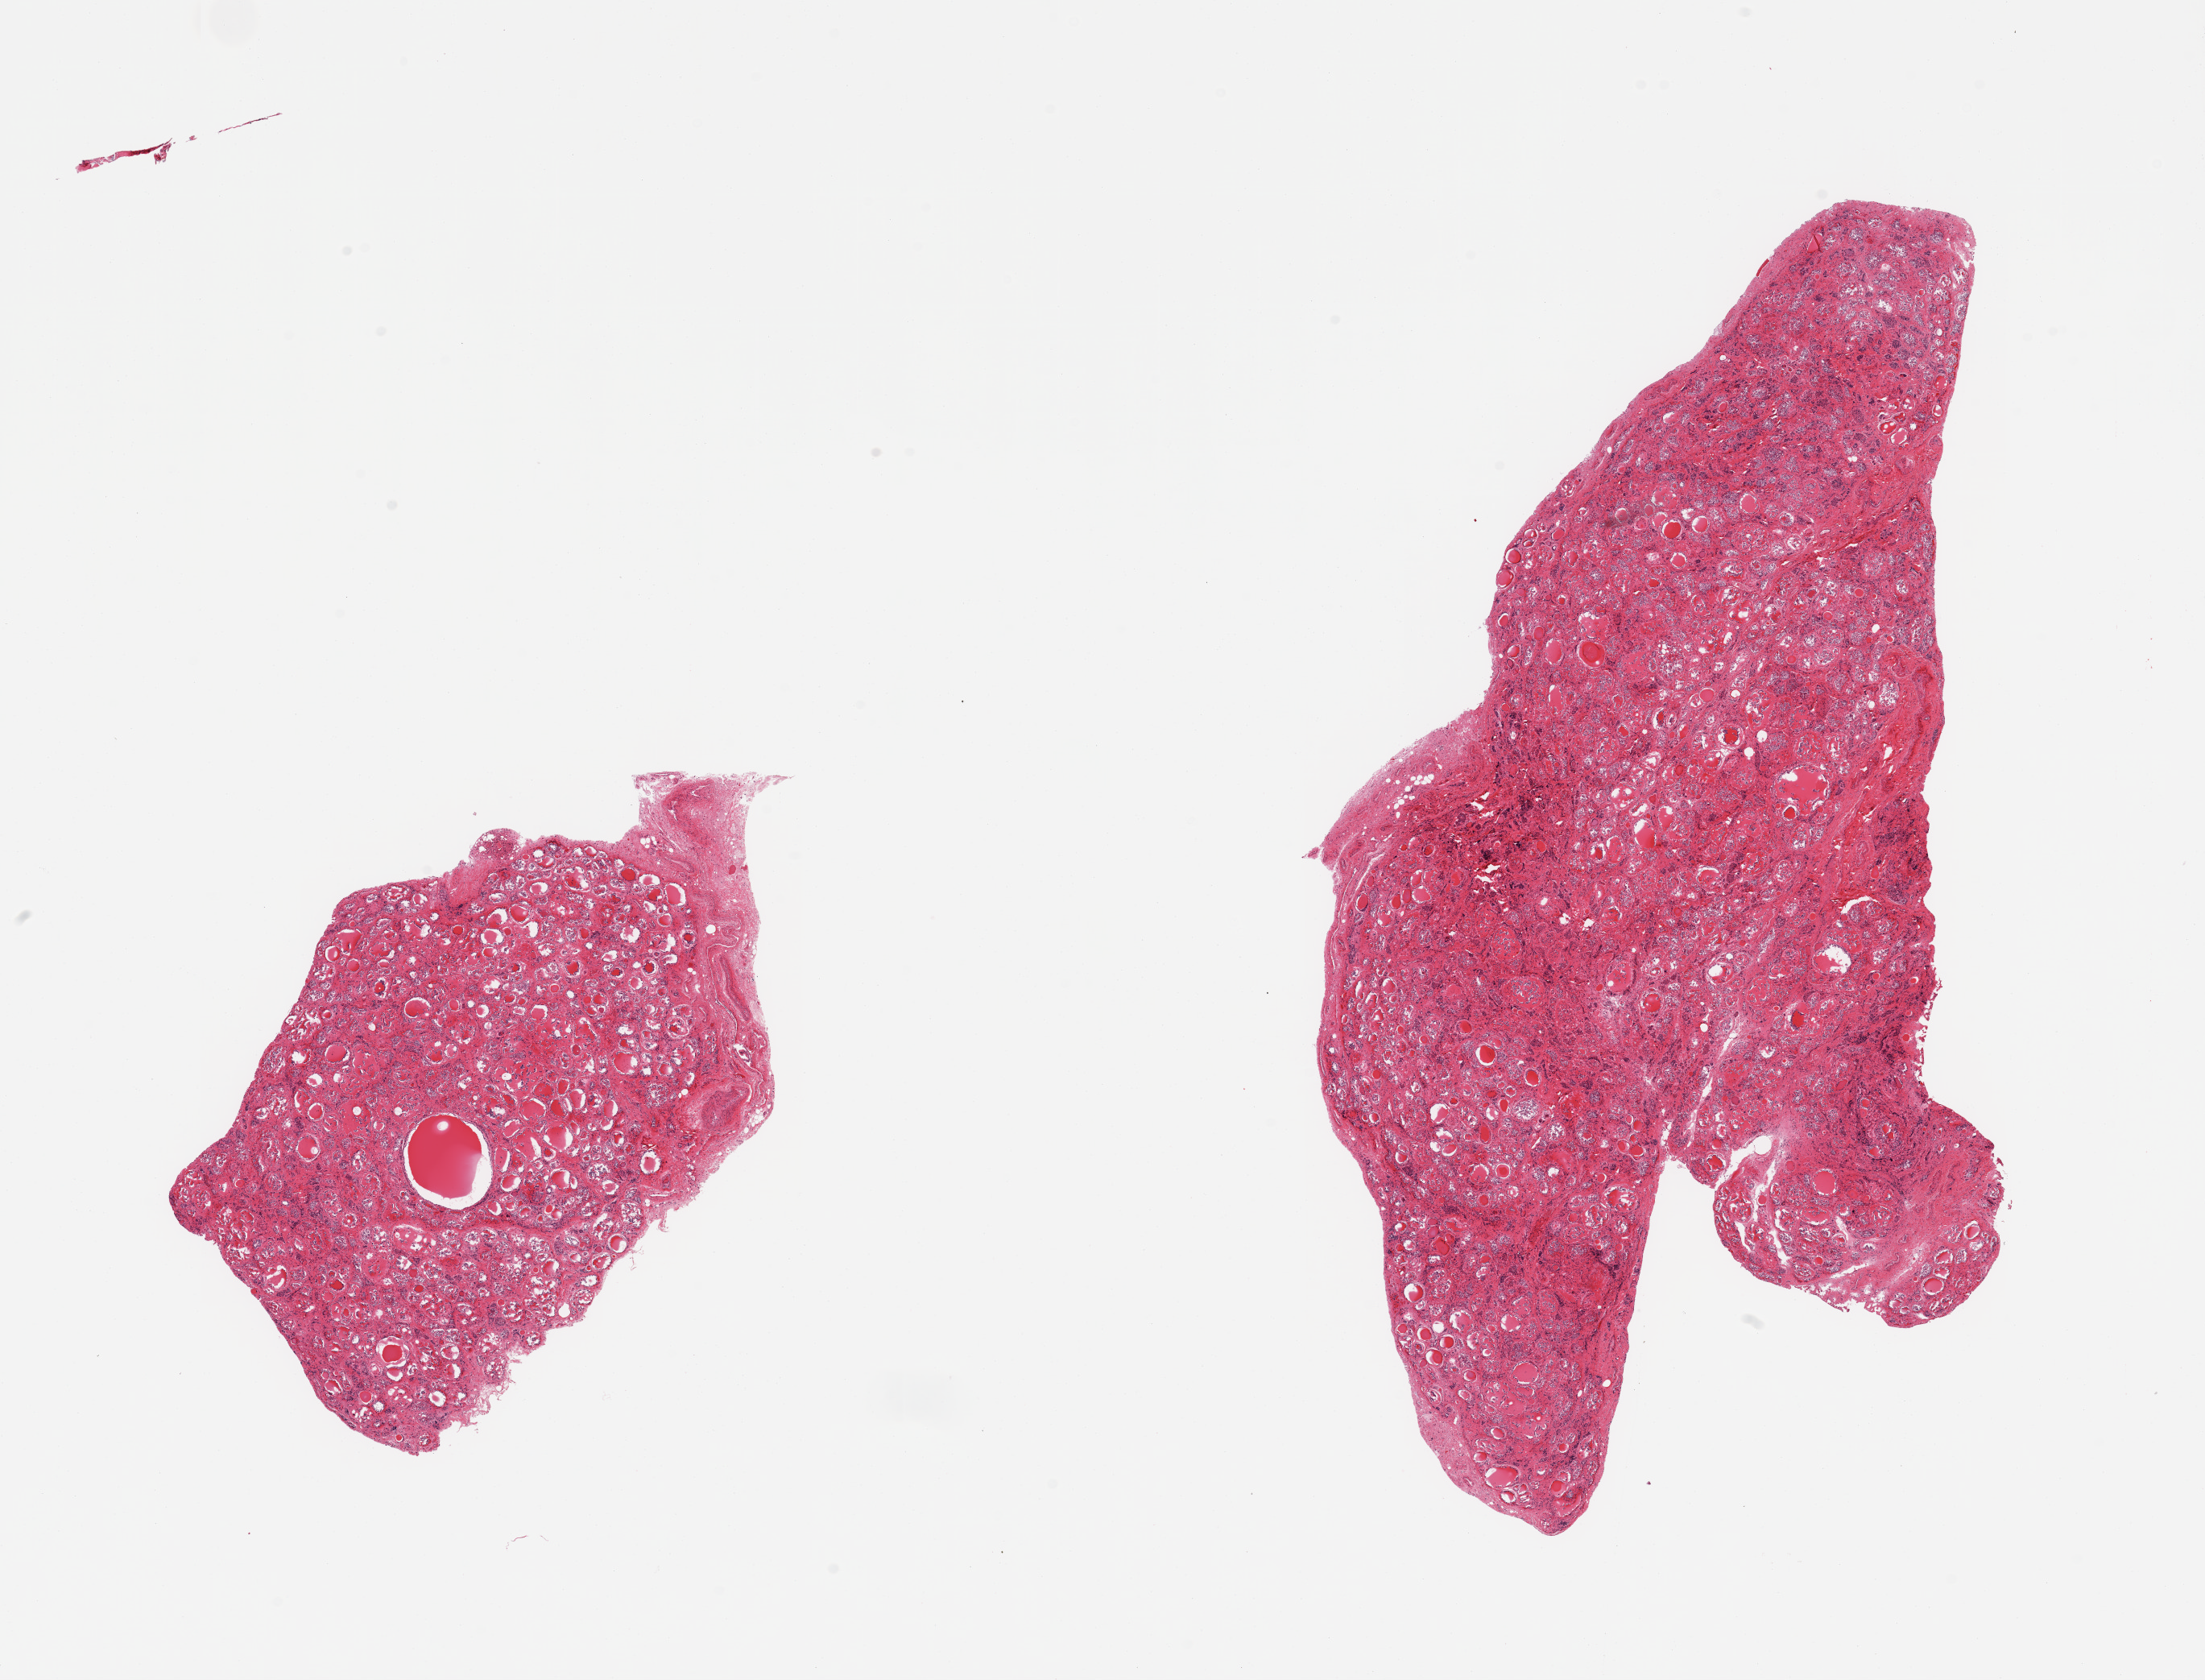
Whole-slide image, hematoxylin and eosin (H&E) stain, shown as a low-resolution overview of the whole scanned area (about 21.7 x 16.5 mm, slide scanned at 20x), PAXgene-fixed, paraffin-embedded tissue, target tissue: thyroid, donor tissue sample. Donor: female.
- reviewer comment on this tissue sample: 2 pieces; some areas are severely autolyzed